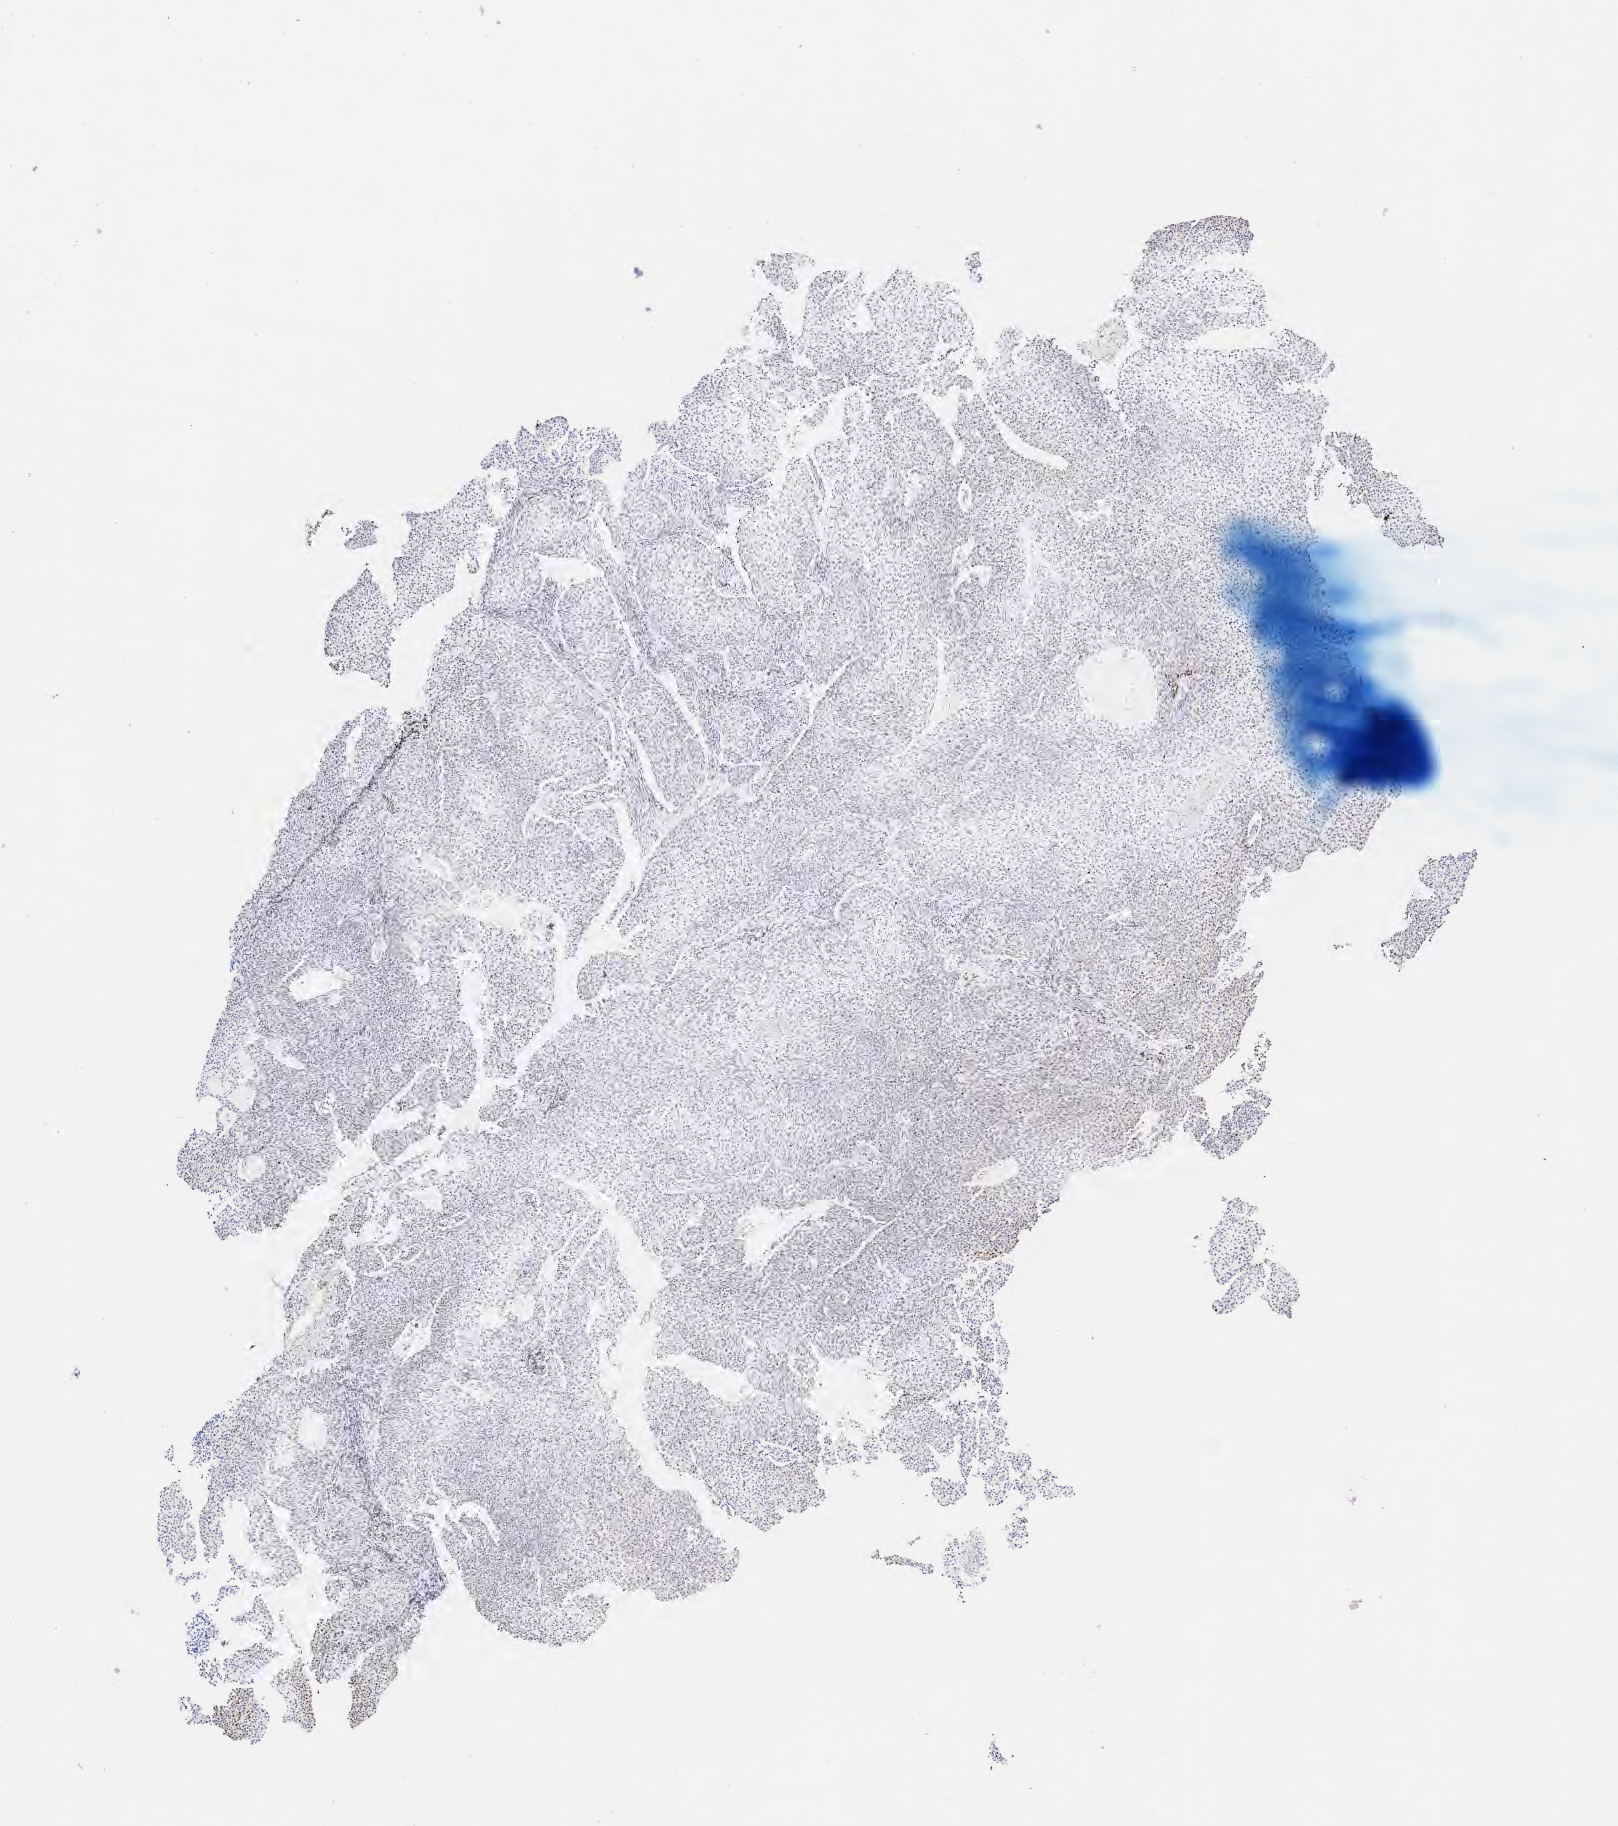
Immunohistochemistry (IHC) whole-slide image stained for p63 — a low-resolution overview of the entire scanned area, about 6.5 x 7.4 mm, tumor tissue, site: cervix. Female patient, age 39 years.
Diagnosis: Squamous cell carcinoma, large cell, nonkeratinizing, NOS.